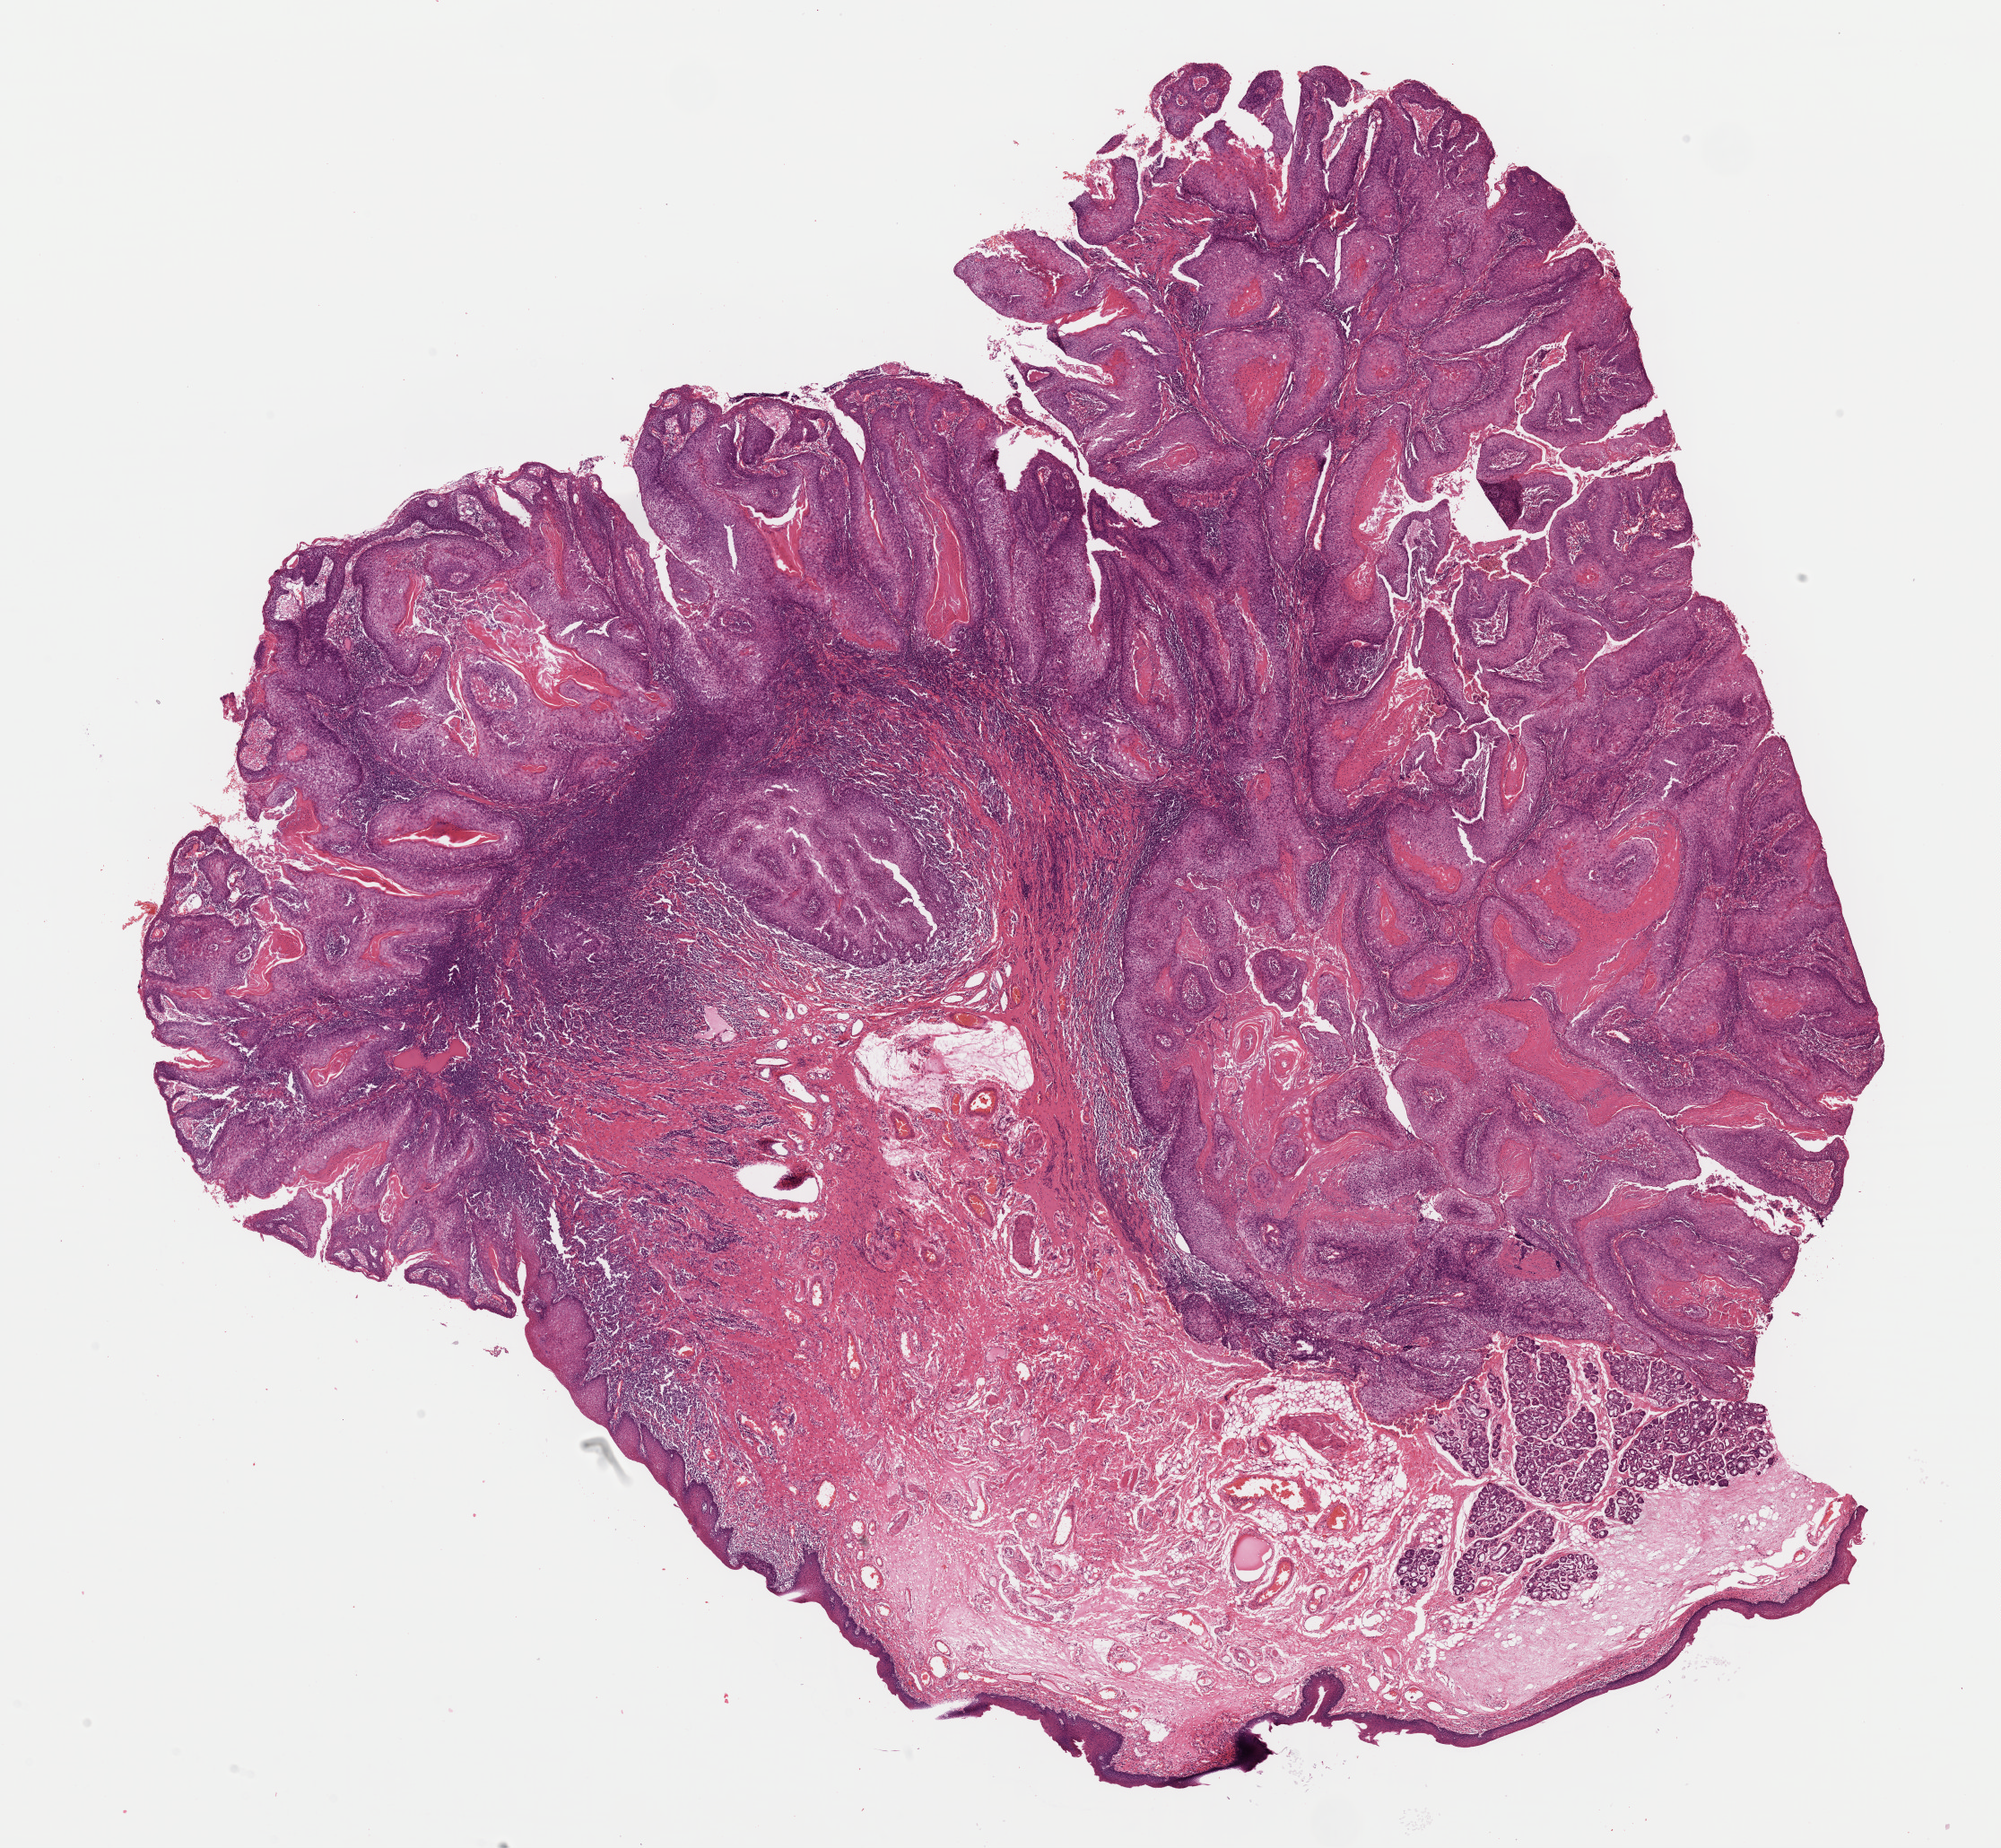
Hematoxylin and eosin (H&E) stained whole-slide image — shown as a low-resolution overview of the whole scanned area (about 17.6 x 16.3 mm, from a 40x scan); FFPE section; sample: primary tumour, head and neck. Male, age 70 years at initial diagnosis. Histologic grade: G1 (well differentiated).
AJCC pathologic stage: IVA (7th edition). Diagnosis: Squamous cell carcinoma, NOS (larynx, NOS).